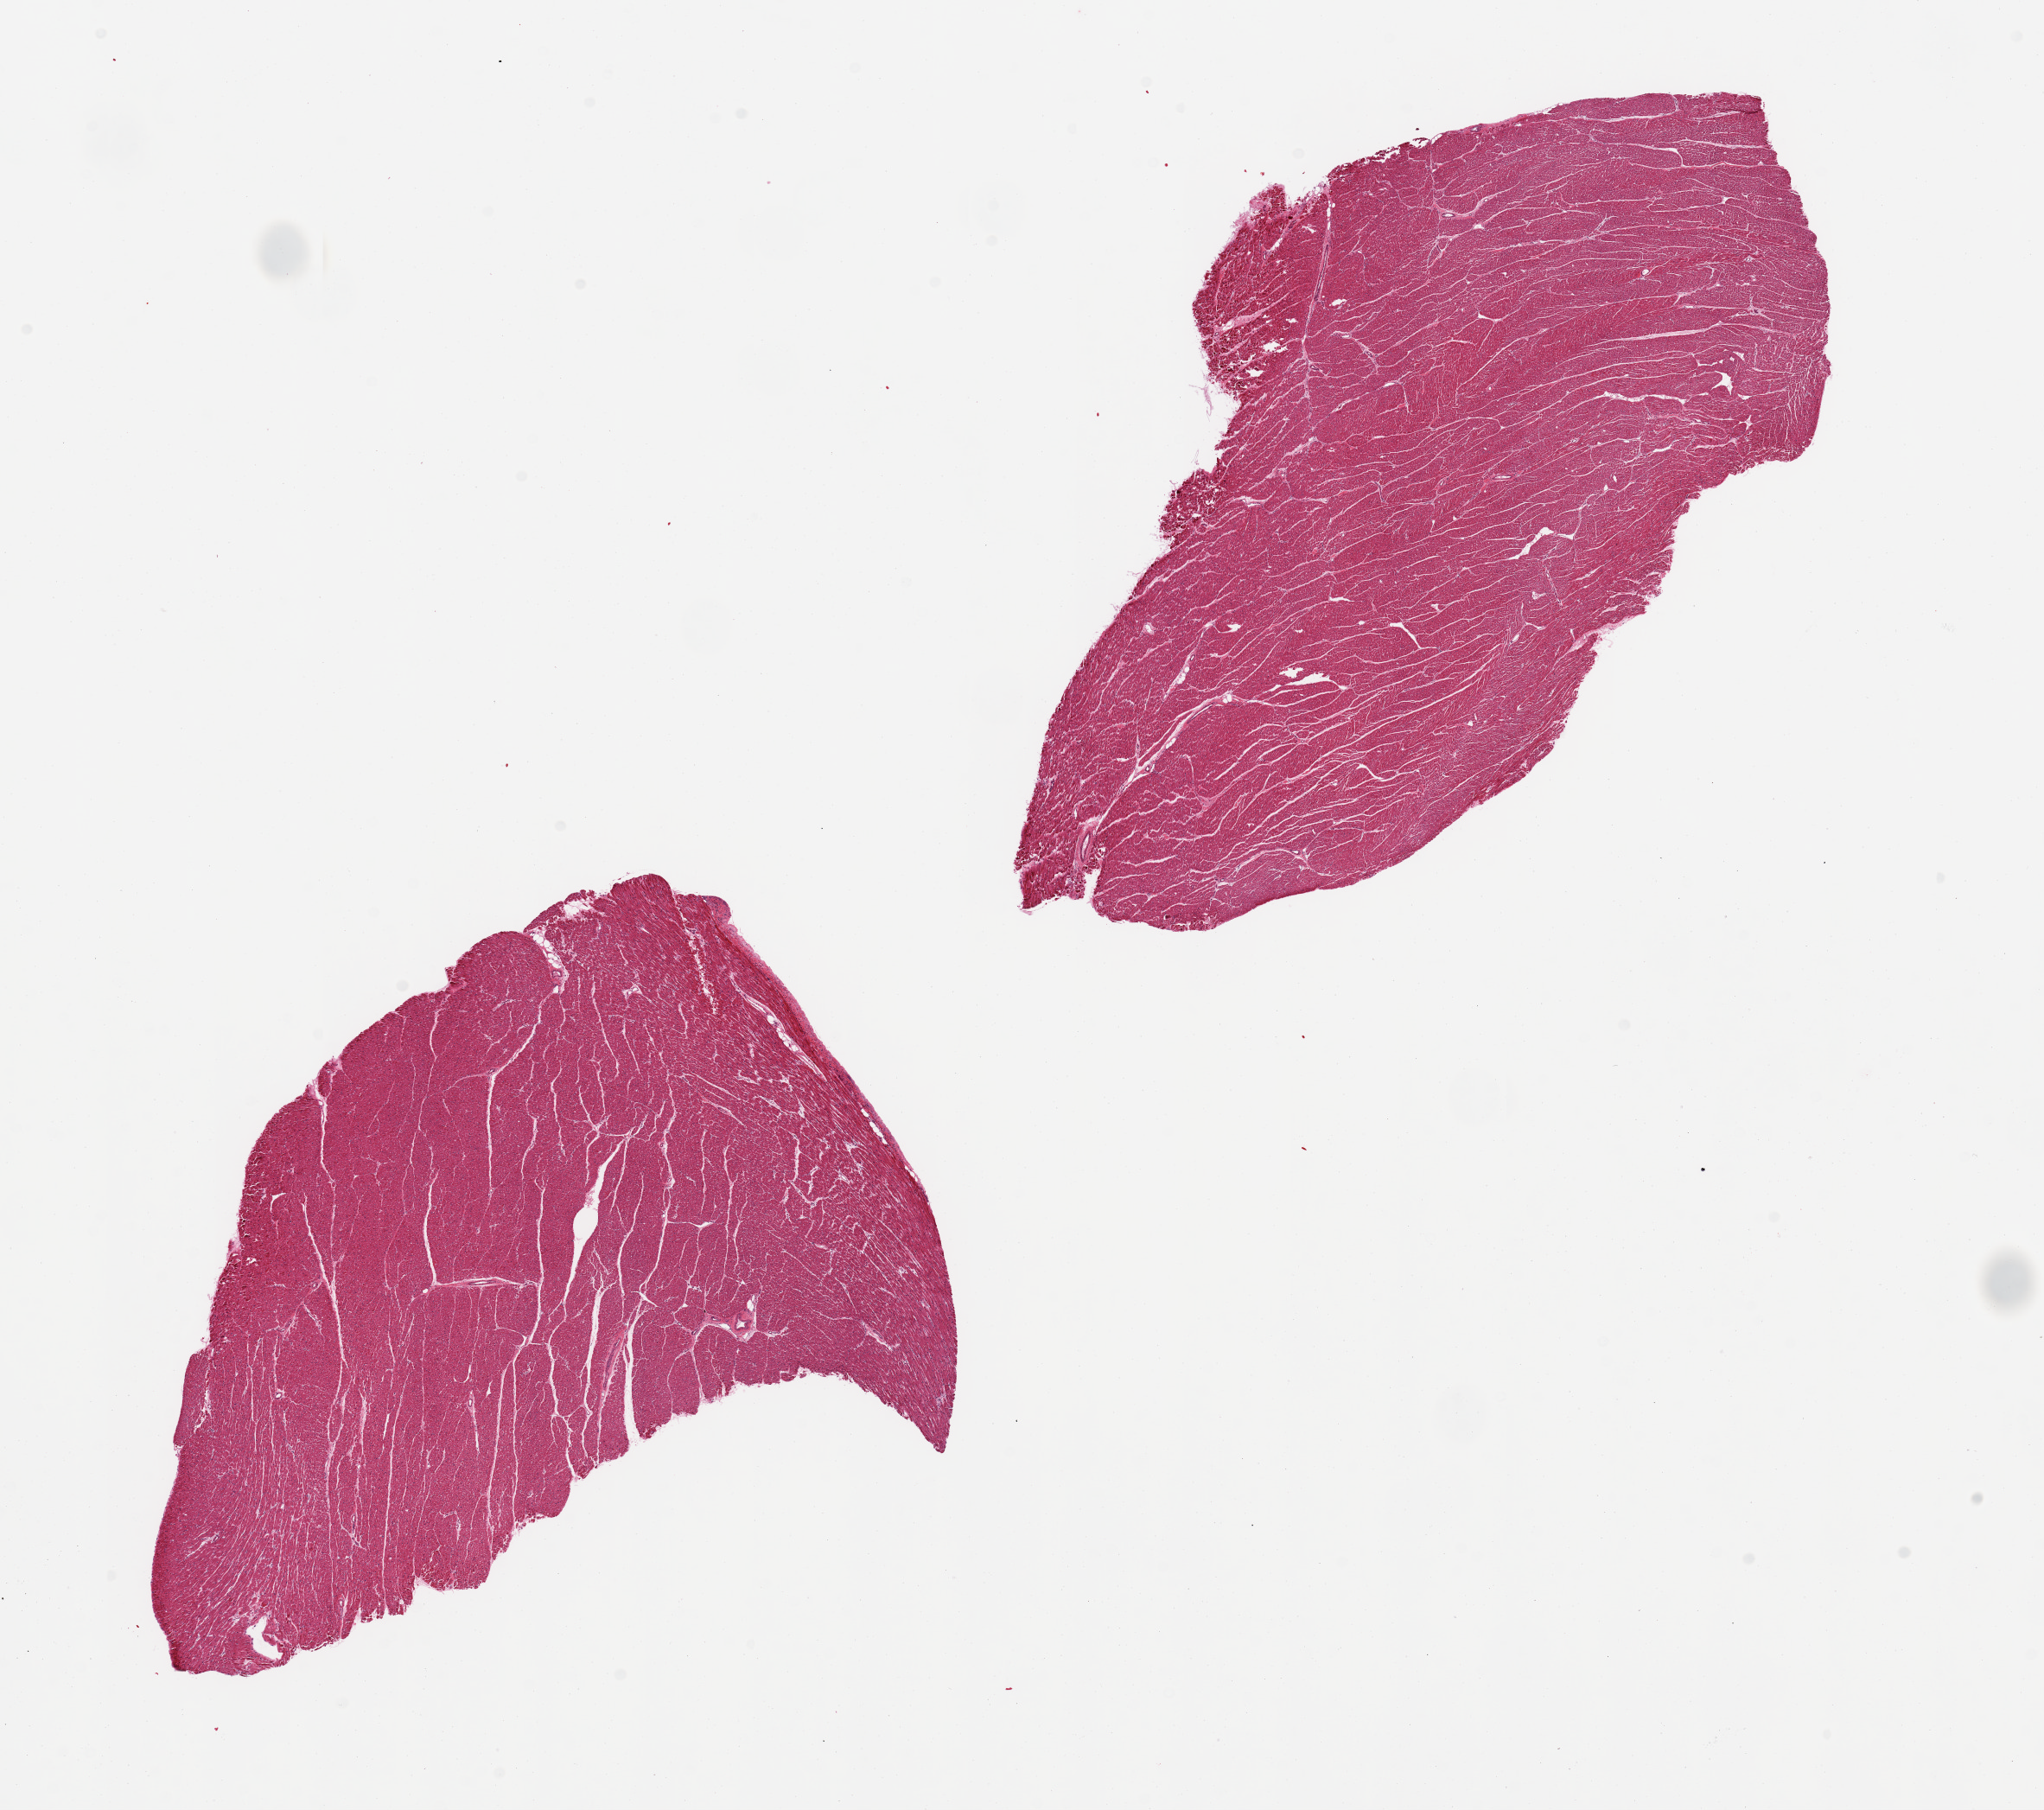
Whole-slide image, haematoxylin and eosin stain, shown as a low-resolution overview of the whole scanned area (about 18.7 x 16.6 mm), PAXgene-fixed, paraffin-embedded tissue, sampled site (target tissue): heart, tissue donor sample.
Review note (as recorded): 2 pieces, no abnormalities.